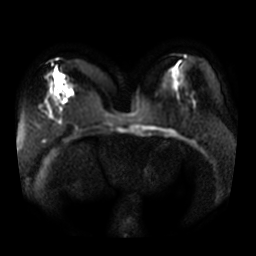
Breast MRI, one axial slice; position 15 of 36 along the scan axis; diffusion-weighted series; image 2 of 4 stored at this slice position (different b-values; order by instance number); 3 T; 5 mm slice thickness; 256 × 256 image matrix, field of view 370 × 370 mm. Female patient.
Outlined on this slice (manually delineated by an expert):
- tumour on diffusion-weighted imaging: bounding box [x1, y1, x2, y2] px = [57, 96, 65, 102]